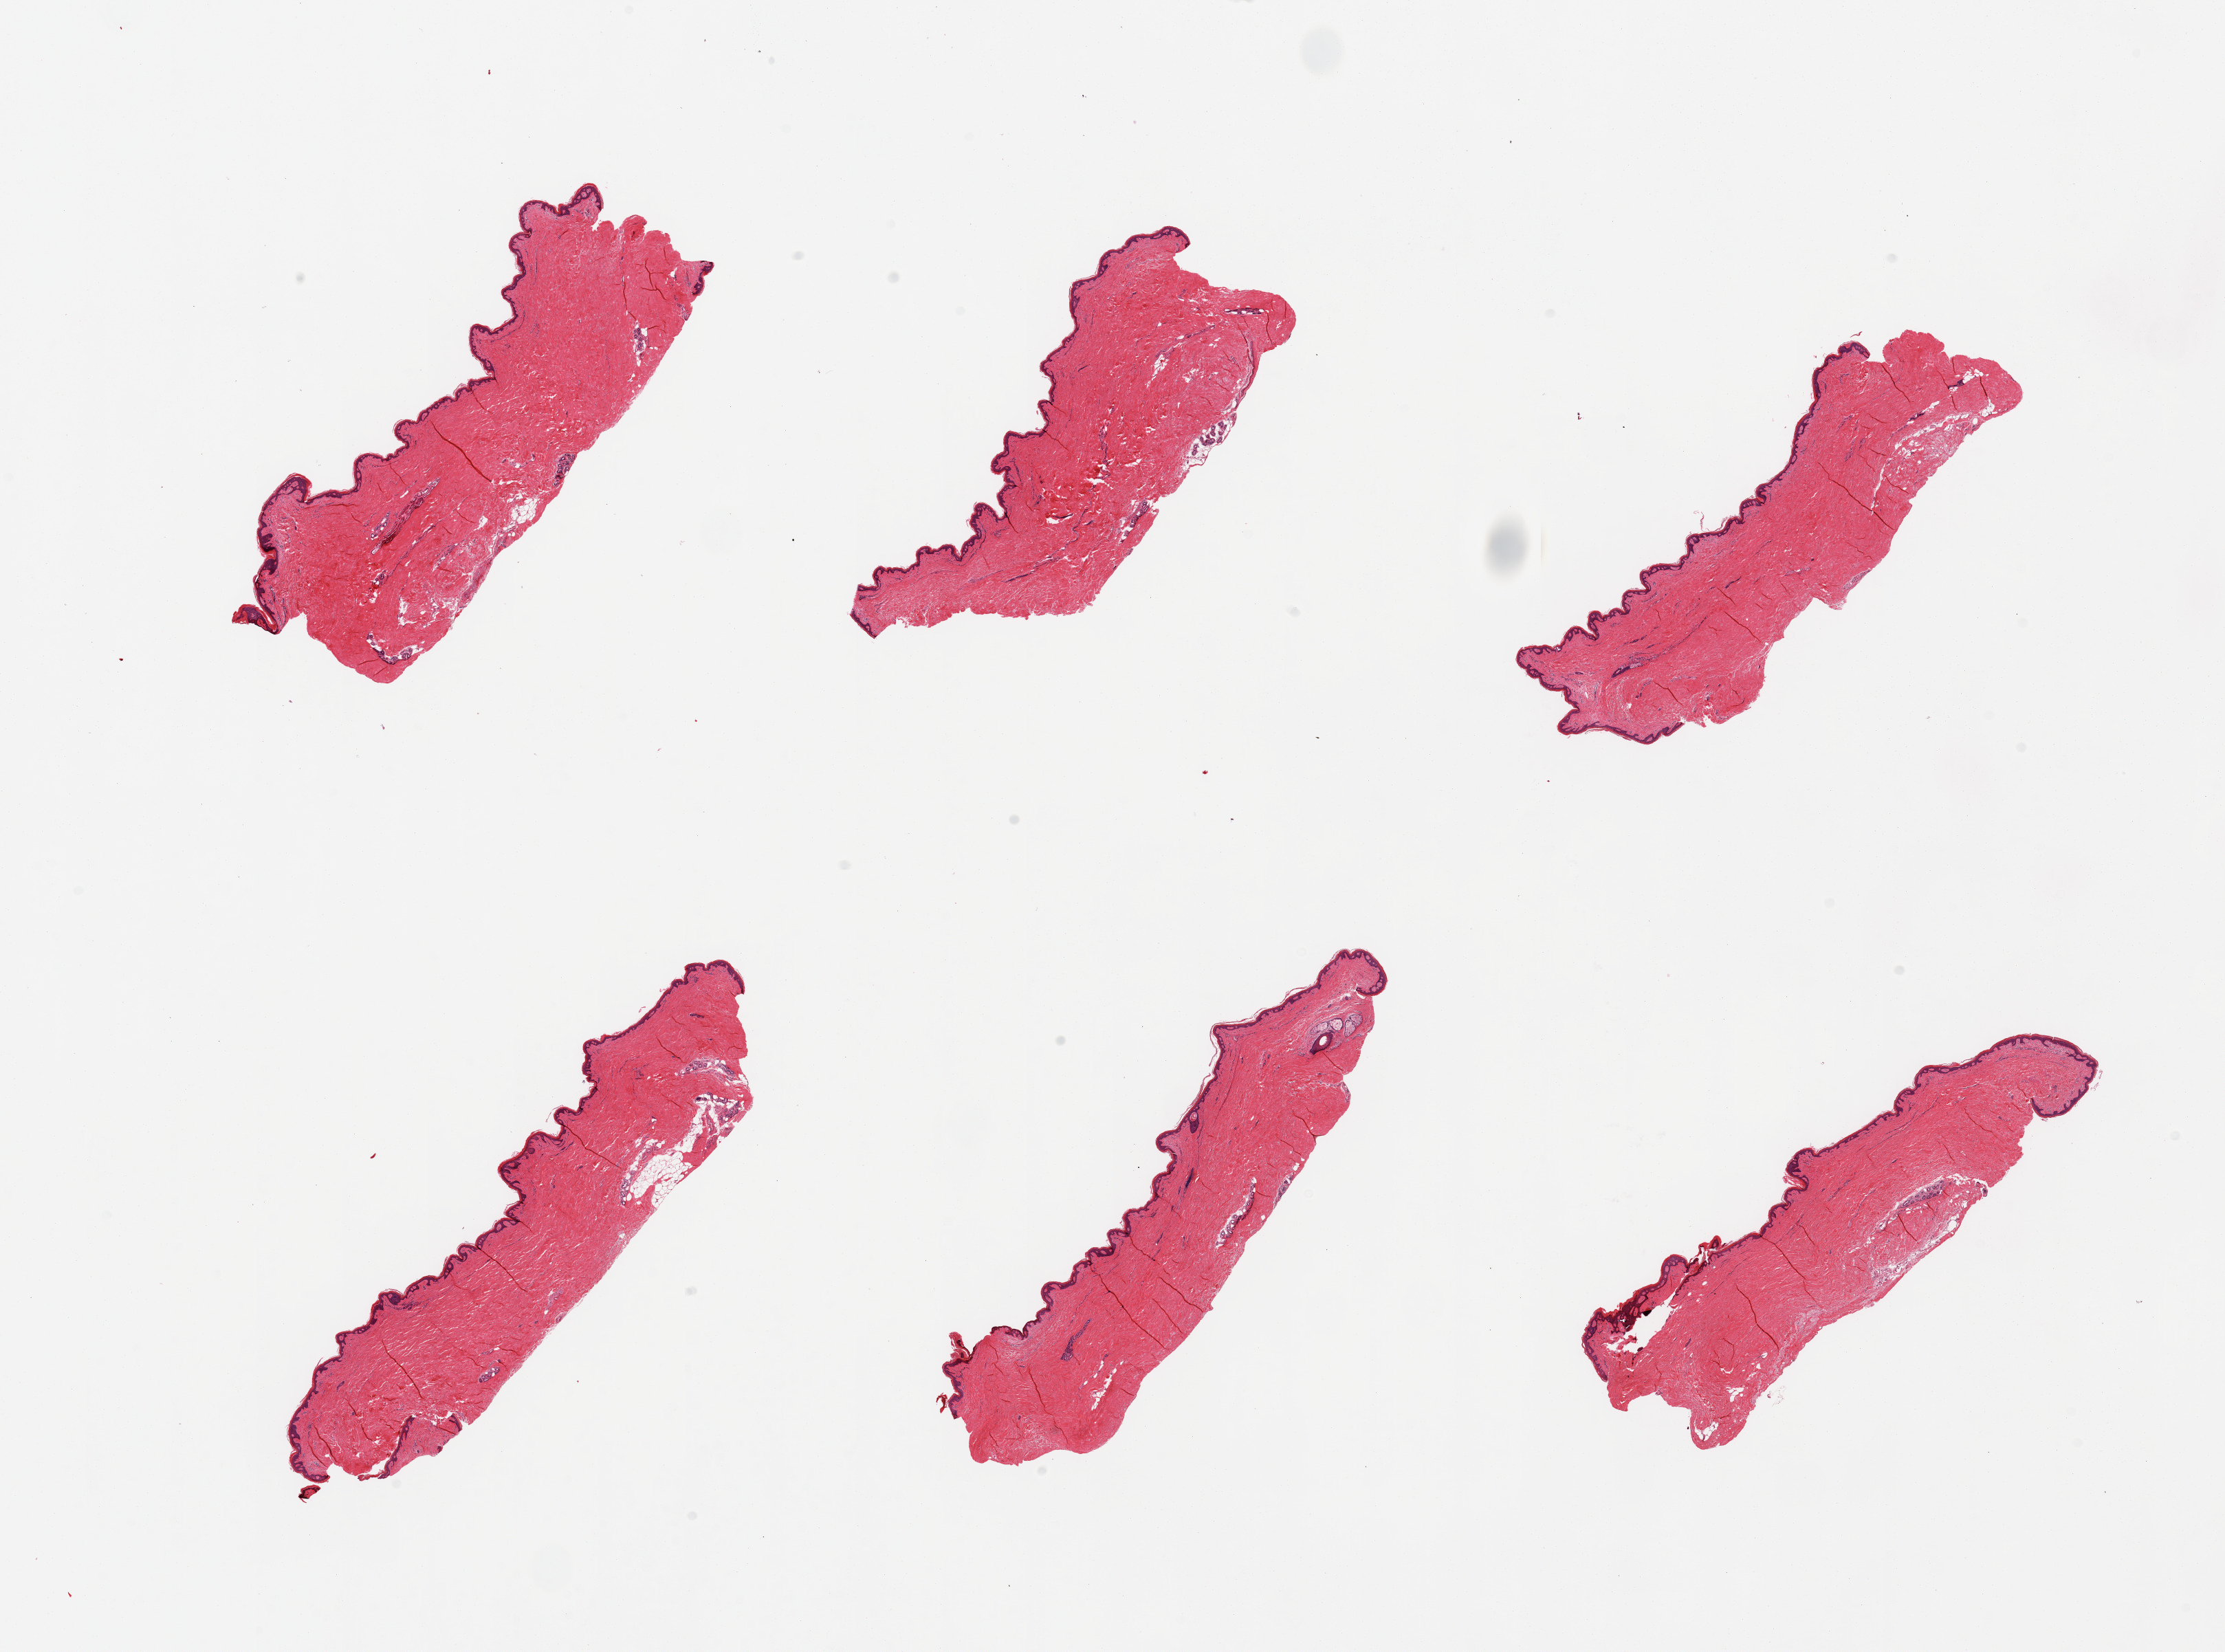
Digitized hematoxylin and eosin (H&E)-stained section — low-resolution overview of the scanned area, about 25.6 x 19.0 mm. PAXgene-fixed paraffin-embedded (PFPE) section. Section of skin of suprapubic region (target tissue). Donor tissue sample. Donor sex: male.
Reviewer comment on this tissue sample: 6 pieces, minimal dermal fat; squamous epithelium is ~15-30 microns.